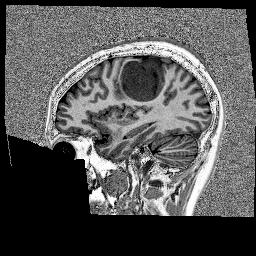
Brain MRI from a brain-tumour surgery series, one sagittal slice; position 55 of 176 along the scan axis; 1 mm slice thickness; 256 × 256 image matrix, field of view 256 × 256 mm. From the clinical record (not read from this slice): histopathology: Glioblastoma; WHO grade: 4; IDH mutation: no; tumour location: Left Frontal.
Annotated regions visible in this slice (manually delineated by an expert):
- tumour: bounding box [x1, y1, x2, y2] px = [118, 58, 175, 105]